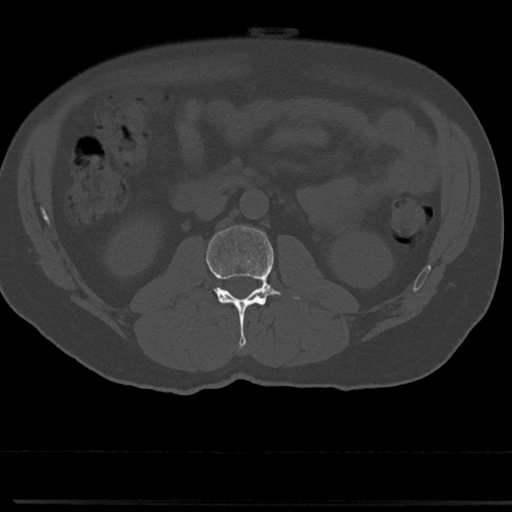
CT including the spine, one axial slice. Position 8 of 817 along the scan axis. Bone window (W 1800 / L 400 HU). 0.5 mm slice thickness. 512 × 512 image matrix, field of view 355 × 355 mm. Male patient, age 61 years. From the clinical record (not read from this slice): primary cancer: prostate.
Annotated regions visible in this slice (semi-automatic segmentation, software-assisted and operator-edited):
- L2 vertebra: bounding box <206,225,300,349> (left, top, right, bottom; pixels)